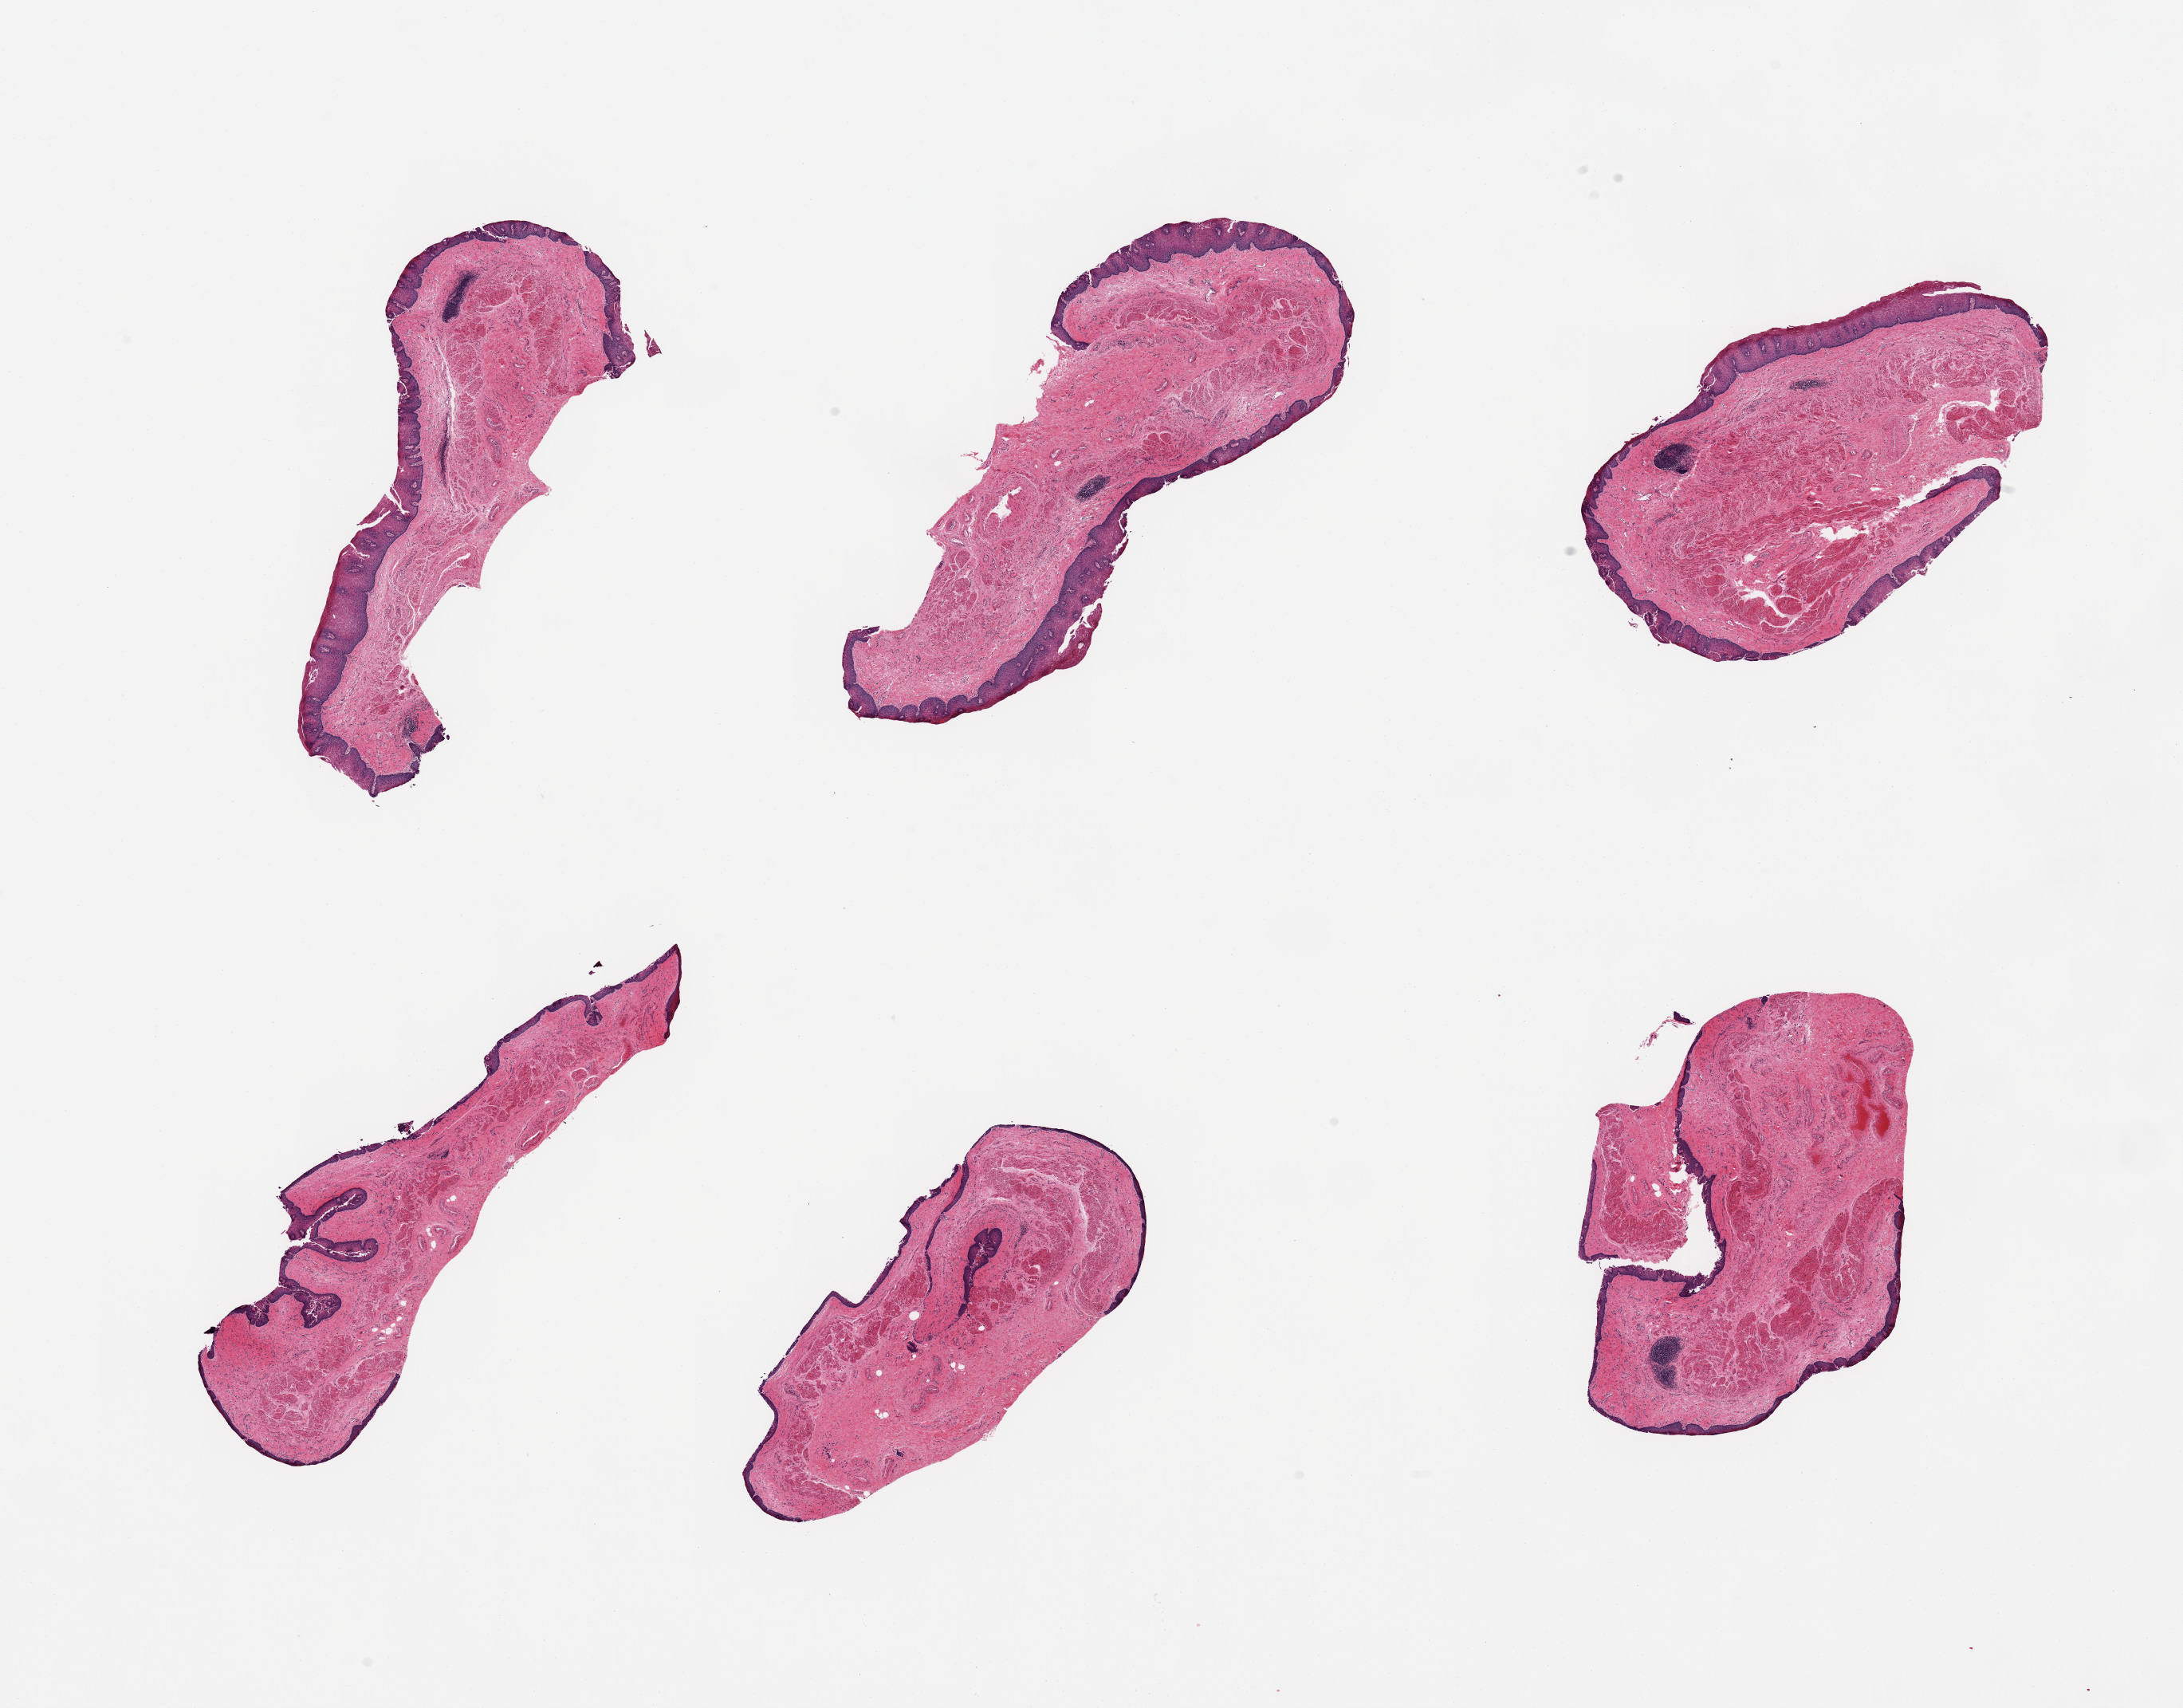
H&E whole-slide image — low-resolution overview of the scanned area, about 21.7 x 16.9 mm (acquisition: 20x scan); PAXgene-fixed paraffin-embedded (PFPE) section; sampled site (target tissue): esophageal mucous membrane; tissue donor sample. Donor sex: male.
- review note (as recorded): 6 pieces, squamous mucosa is ~0.35mm, ~10-15% thickness